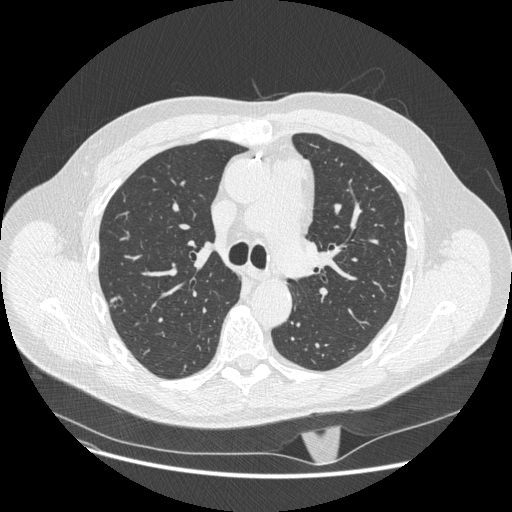
Chest CT (low-dose screening protocol), one axial image, second annual screen, lung window (W 1500 / L -600 HU), slice 79 of 247 in the series. Male, age 62 years at enrolment. Current smoker at enrolment.
Expert reader's lesion annotation, bounding box [x1, y1, x2, y2] px = [96, 288, 132, 317]. The exam's reader record, not a measurement of the box and not confirmed to be the same lesion: non-calcified nodule or mass ≥4 mm, right upper lobe, 11 × 7 mm, smooth margins, pre-existing on the prior screen: yes.